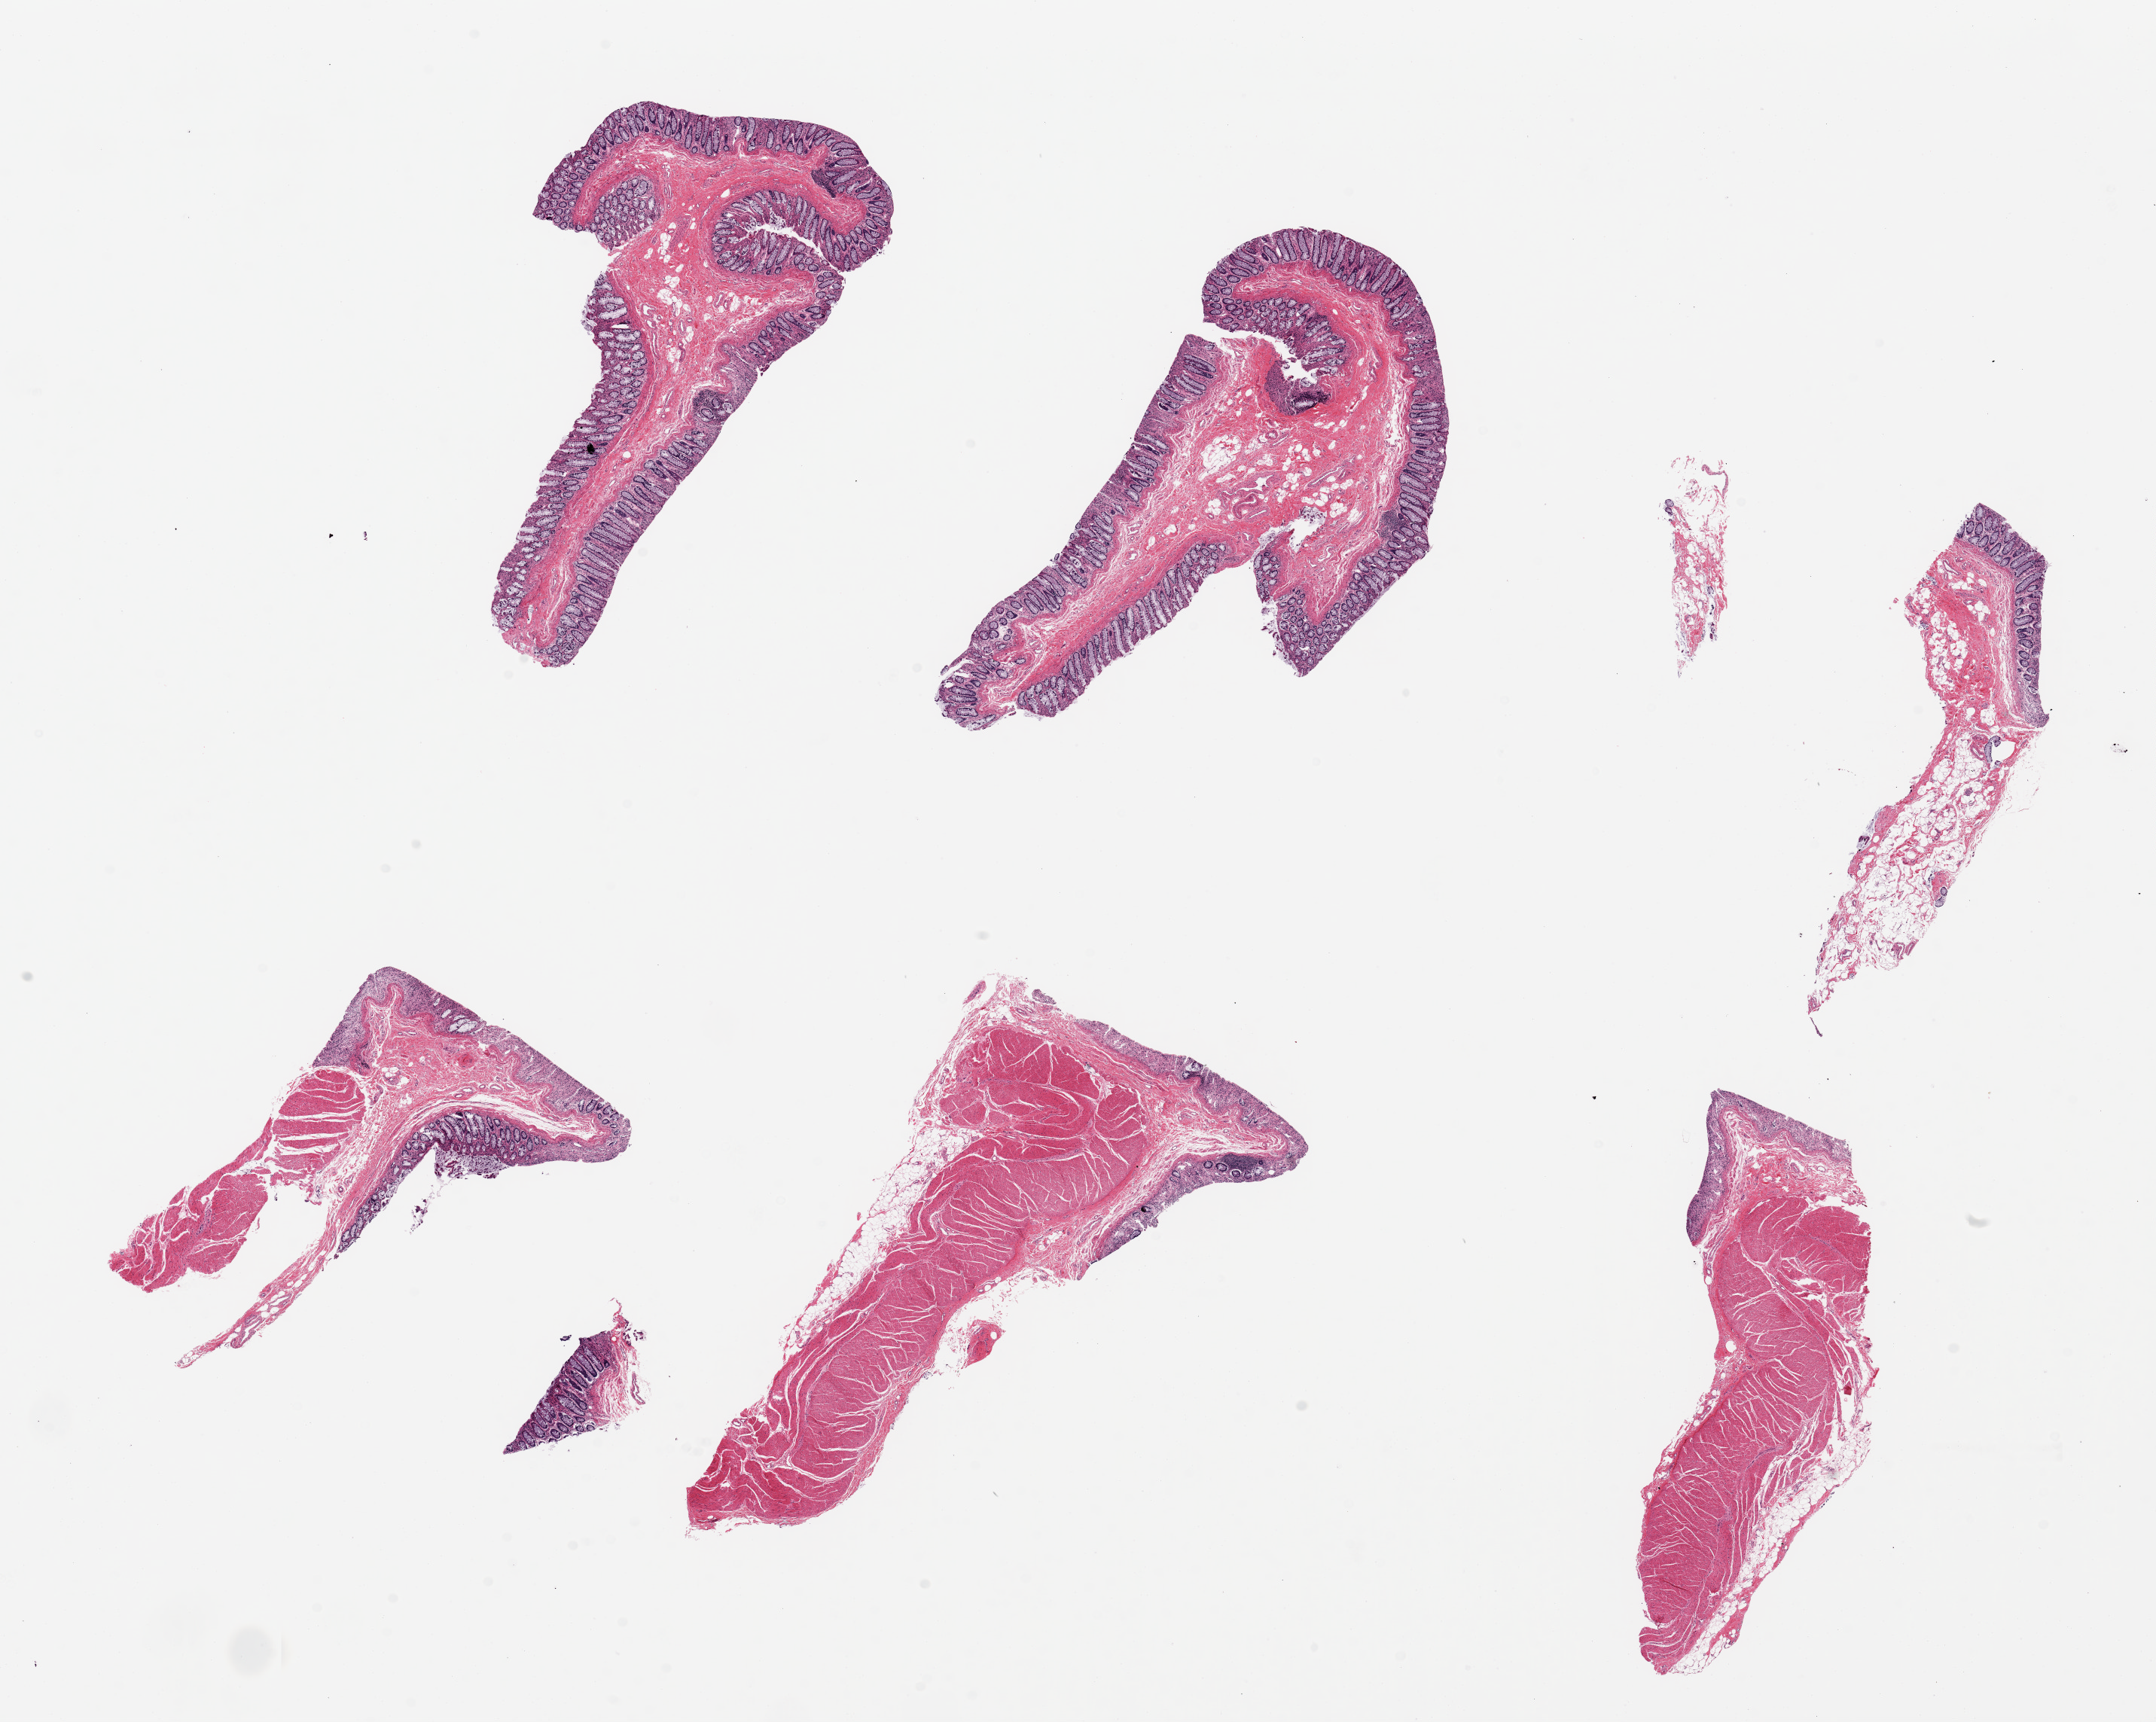
Whole-slide image, hematoxylin and eosin (H&E) stain, low-resolution overview of the scanned area, about 22.6 x 18.1 mm. PAXgene-fixed, paraffin-embedded tissue. Target tissue: sigmoid colon. Tissue donor sample. Male donor.
Review note (as recorded): 6 pieces, up to 7x3mm; all have mucosa, 3 have muscle; Muscle is slightly autolyzed, mucosa is moderately autolyzed.